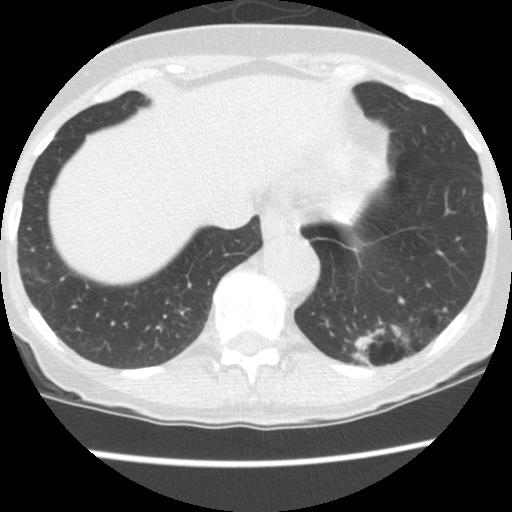
Low-dose screening chest CT, one axial slice; position 30 of 130 along the scan axis; reconstruction kernel STANDARD; lung window (W 1500 / L -600 HU); 512 × 512 image matrix, field of view 290 × 290 mm.
Structures marked on this image (outlined manually by an expert reader):
- lesion 1 (tumor, lower lobe of left lung): bounding box <351,326,380,369> (left, top, right, bottom; pixels)